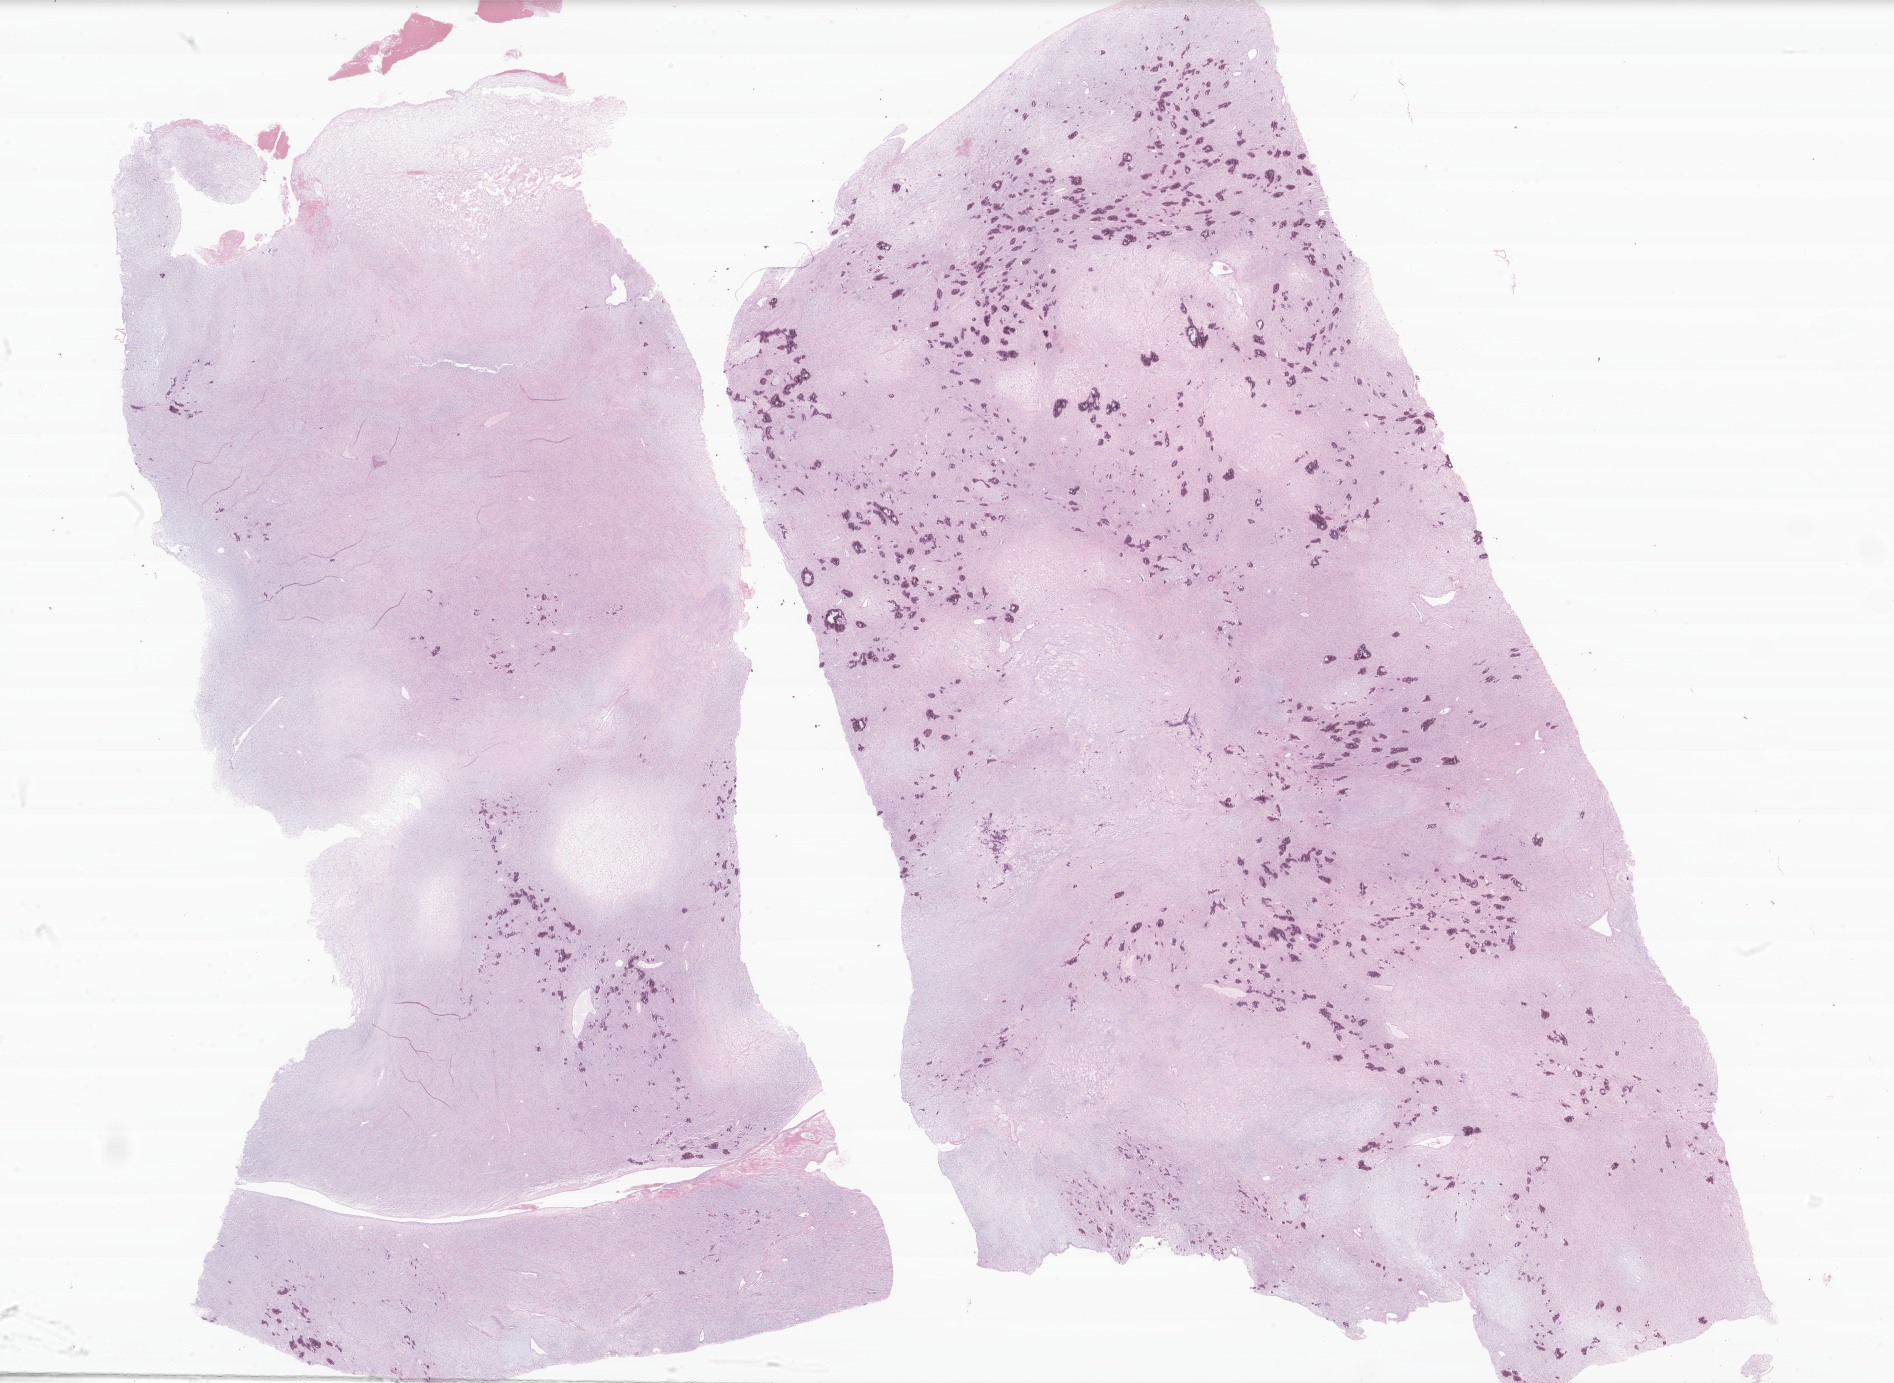
H&E whole-slide image of tumor tissue from the fallopian tube — low-resolution overview of the scanned area, about 31.9 x 23.3 mm; FFPE section. Patient: female, age 180 months (15 years).
Diagnosis (ICD-O-3 morphology term): Sclerosing stromal tumor.